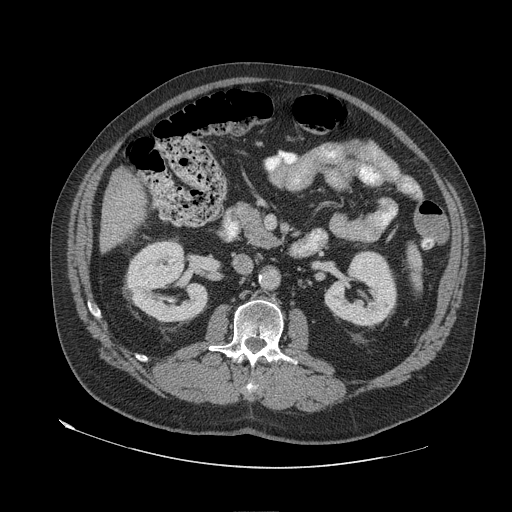
Contrast-enhanced abdominal CT (liver protocol), one axial slice. Slice 16 of 79 in the series (ordered by position). Soft-tissue window (W 400 / L 40 HU). 2.5 mm slice thickness. 512 × 512 image matrix. From the clinical record (not read from this slice): diagnosis: hepatocellular carcinoma (patient treated with transarterial chemoembolisation; whether this scan precedes or follows treatment is not stated here); TNM stage (as recorded): Stage-IVA; Child-Pugh class: A; tumour nodularity: multinodular.
Outlined on this slice (semi-automatically segmented with operator editing):
- liver parenchyma outside the tumour (the mass and vessels are separate outlines, so this box may not span the whole liver): box from (x=100, y=168) to (x=146, y=252) px